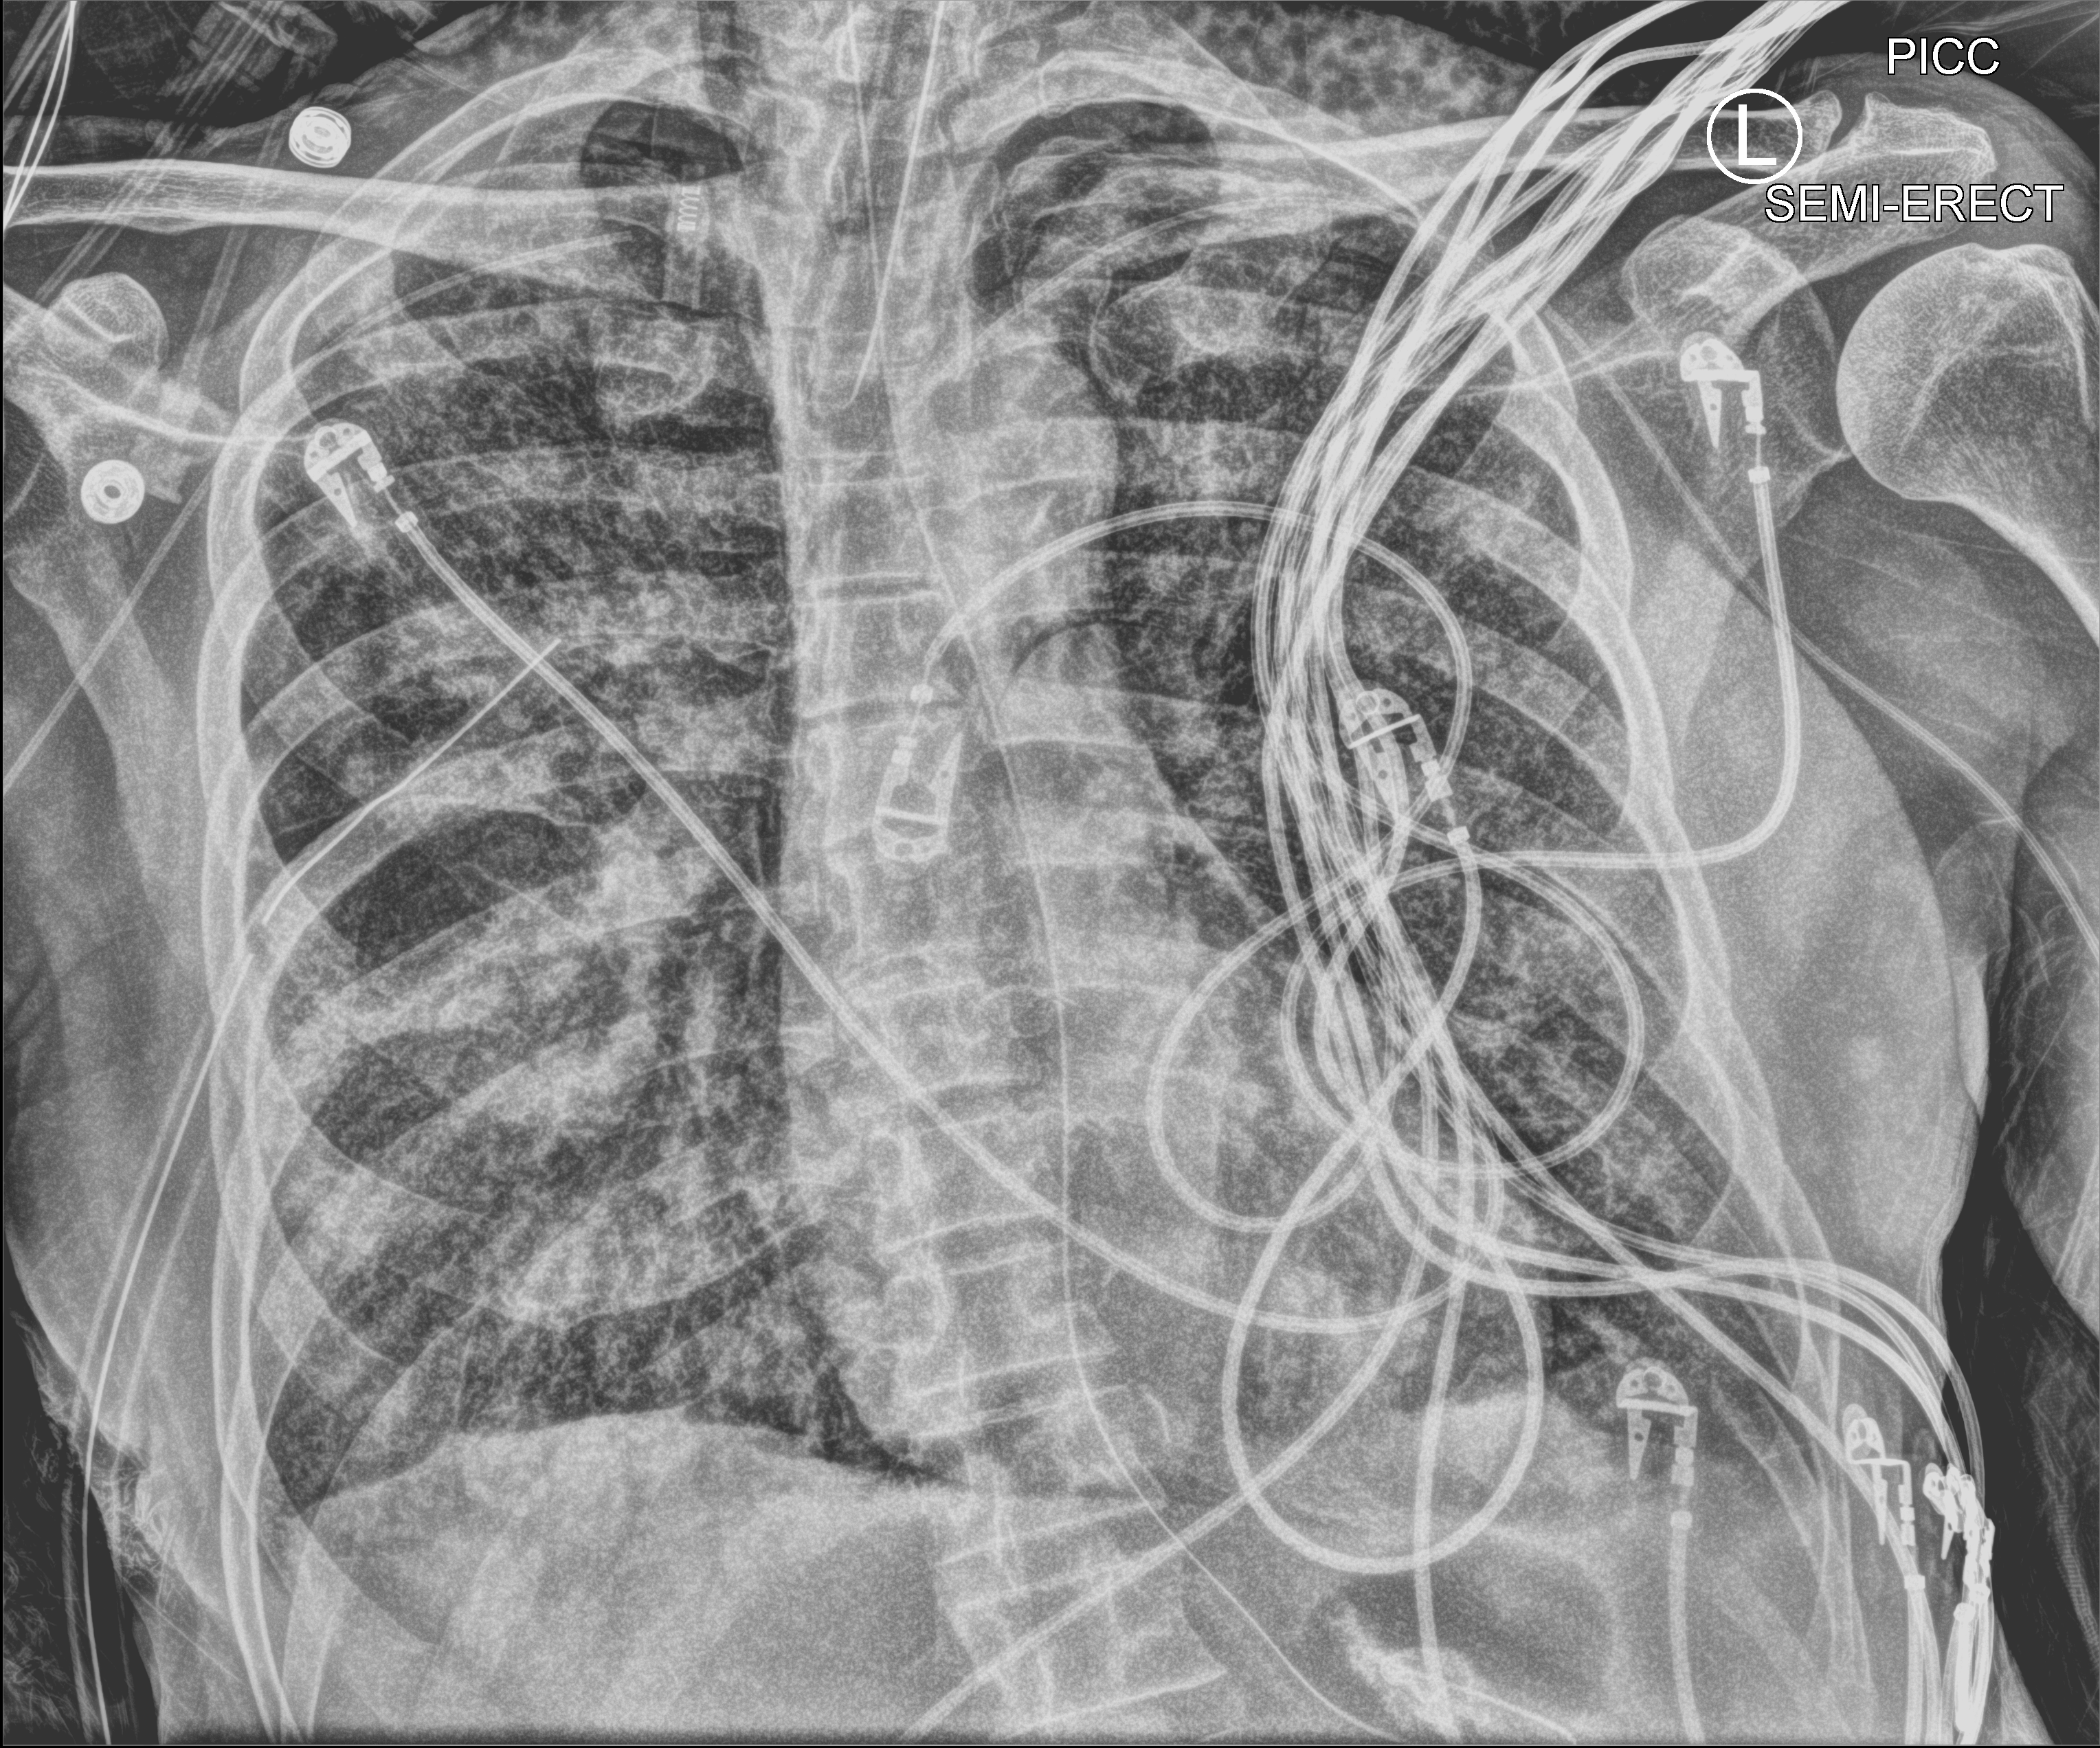
Portable chest radiograph, anteroposterior (AP) projection. Patient hospitalised with COVID-19; male, aged 60–74 years.
Hospital-stay facts (about this admission, not read from this image; timing relative to this image not recorded): mechanically ventilated during this hospital stay: yes; hypertension (admission record): no.